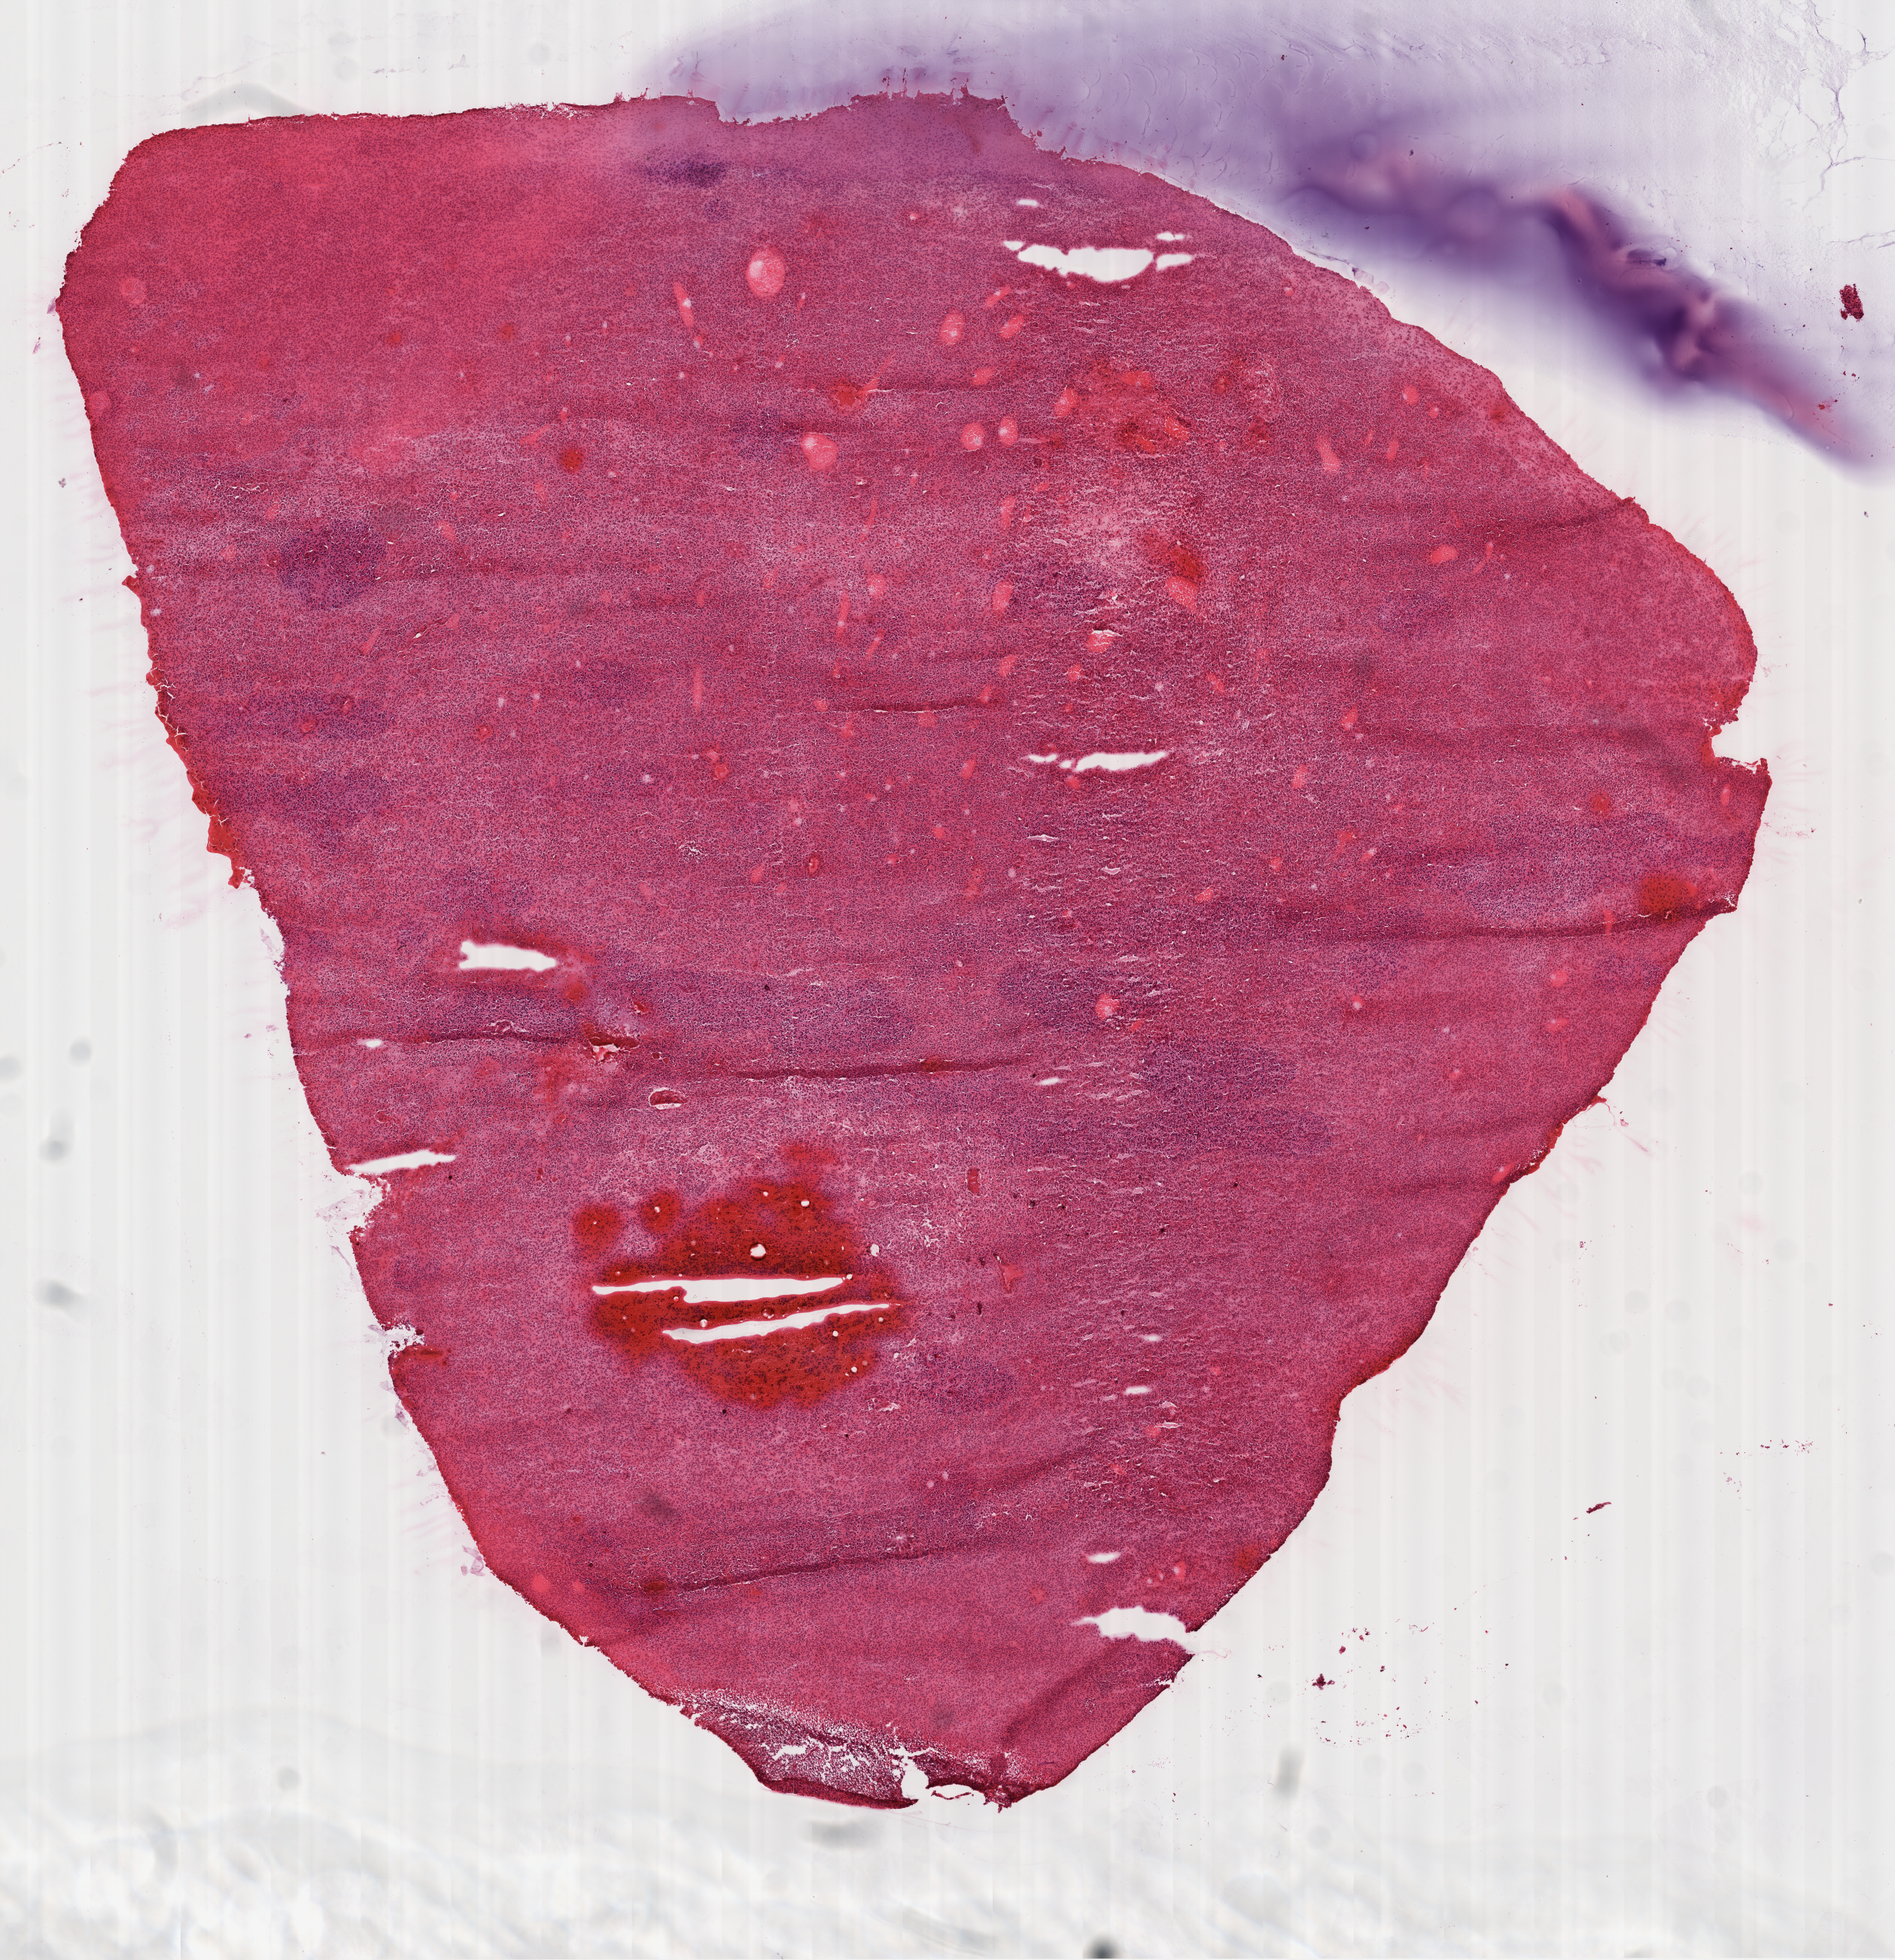
Whole-slide histology image, H&E-stained — a low-resolution overview of the entire scanned area, about 10.2 x 10.5 mm. Frozen section. Sample: primary tumour, brain. Patient: male, age at initial diagnosis 52 years. Slide review estimates, as recorded: tumour cells 95%, tumour nuclei 100%, normal cells 0%, stromal cells 0%, necrosis 5%.
Pathologic diagnosis: Glioblastoma.